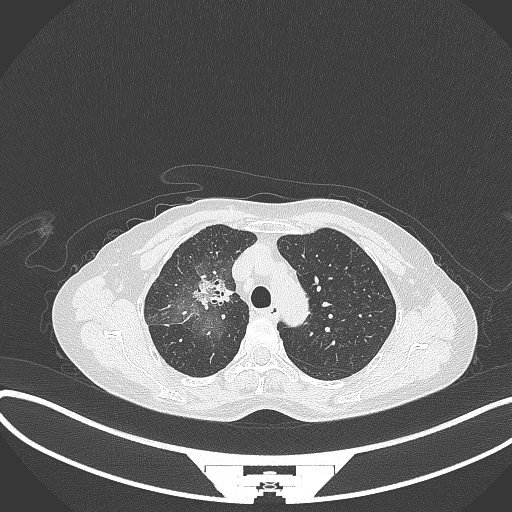
Chest CT, one axial slice; position 235 of 284 along the scan axis; reconstruction kernel B70f; 120 kVp; lung window (W 1500 / L -600 HU); 512 × 512 image matrix, field of view 400 × 400 mm. Female patient, age 59 years. Case-level facts recorded for this patient, not image findings: clinical TNM (as recorded): T3 N0 M0.
Structures marked on this image (bounding box drawn by a radiologist):
- lung tumour (recorded histology: adenocarcinoma): bounding box (x1, y1, x2, y2) in pixels: (187, 268, 234, 310)